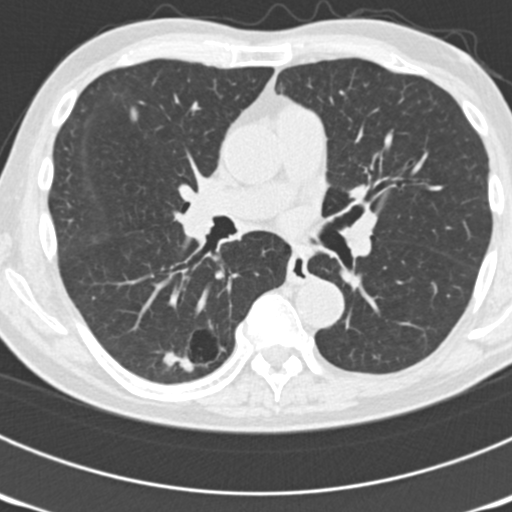
Low-dose screening chest CT, axial slice, third screening round (two years after baseline), lung window (W 1500 / L -600 HU), 2 mm slice thickness, standard (soft-tissue) reconstruction kernel (B30f), 512 × 512 image matrix, field of view 300 × 300 mm. Male, age 70 years at enrolment. Current smoker at enrolment.
Expert-annotated lung lesion, bounding box (x1, y1, x2, y2) in pixels: (146, 306, 238, 385). The screening reader recorded 3 non-calcified nodules or masses ≥4 mm on this exam (right upper lobe, left upper lobe, right lower lobe); which of them this box marks is not recorded. Official screen result: positive, other. Later outcome: lung cancer diagnosed 14 days after this screen — bronchiolo-alveolar adenocarcinoma, NOS, right lower lobe, poorly differentiated (G3), stage IB (AJCC 6th edition), 30 mm at pathology.